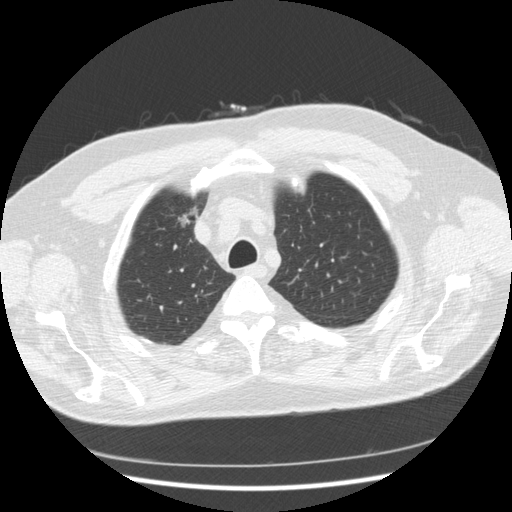
Low-dose screening chest CT, axial slice. Second screening round (one year after baseline). Lung window (W 1500 / L -600 HU). 512 × 512 image matrix, field of view 360 × 360 mm. Male participant, aged 66 years at enrolment. Former smoker at enrolment.
Lesion marked by an expert reader, bounding box (x1, y1, x2, y2) in pixels: (157, 200, 209, 241). No non-calcified nodule or mass ≥4 mm was recorded by the screening reader at this exam. Participant outcome: lung cancer diagnosed 603 days after this screen (after the third annual screen) — bronchiolo-alveolar adenocarcinoma, NOS, right upper lobe, moderately differentiated (G2), stage IA (AJCC 6th edition), 12 mm at pathology.